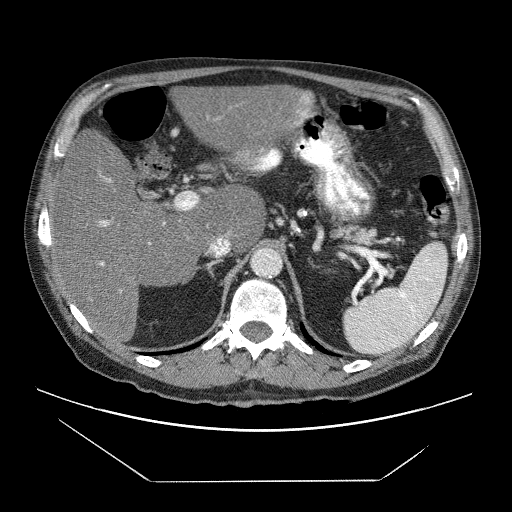
Contrast-enhanced abdominal CT (liver protocol), one axial slice; slice 38 of 83 in the series (ordered by position); reconstruction kernel STANDARD; 120 kVp; soft-tissue window (W 400 / L 40 HU); 512 × 512 image matrix, field of view 420 × 420 mm. Case-level facts recorded for this patient, not image findings: diagnosis: hepatocellular carcinoma (patient treated with transarterial chemoembolisation; whether this scan precedes or follows treatment is not stated here); TNM stage (as recorded): Stage-IVB; Child-Pugh class: B; tumour differentiation: poorly differentiated; tumour nodularity: uninodular.
Outlined on this slice (semi-automatic segmentation, software-assisted and operator-edited):
- liver parenchyma outside the tumour (the mass and vessels are separate outlines, so this box may not span the whole liver): box from (x=50, y=84) to (x=312, y=342) px
- liver vessels: (x=99, y=95)–(x=310, y=266)